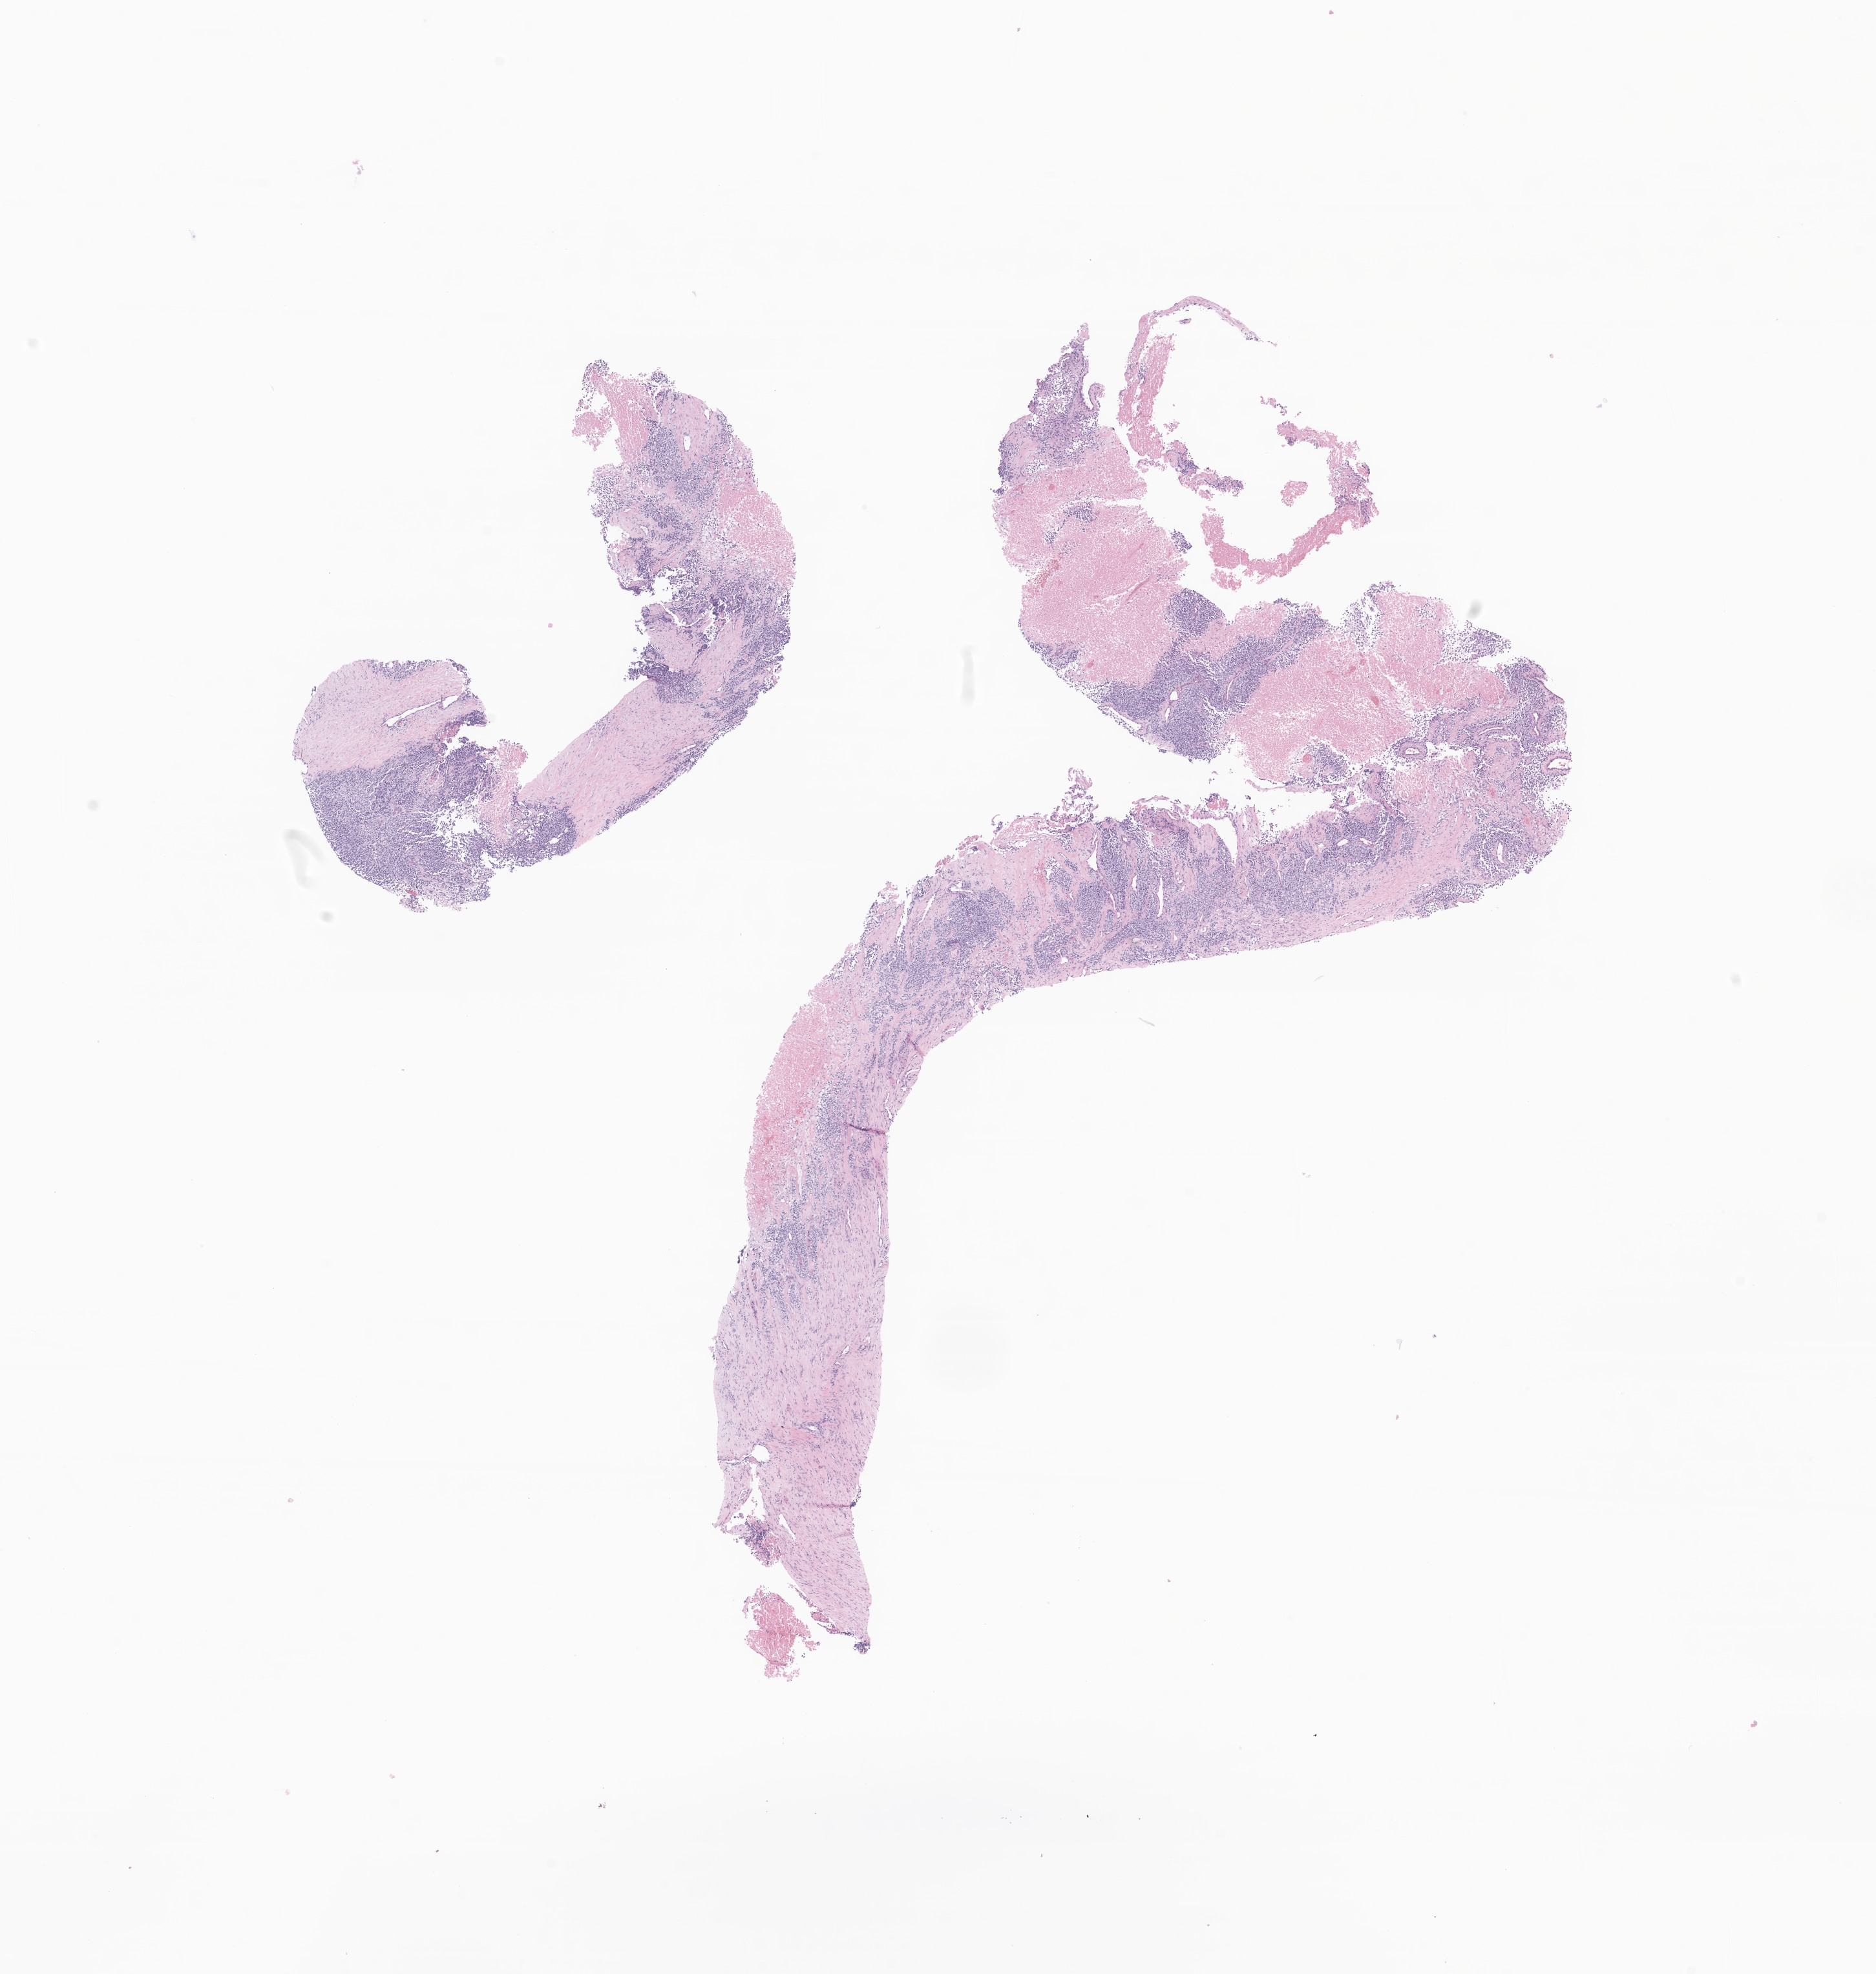
Haematoxylin and eosin whole-slide image of tumor tissue from the soft tissue of upper extremity — whole scanned area (about 12.2 x 12.9 mm) shown as a low-resolution overview. Formalin-fixed paraffin-embedded section. Patient female; age 212 months.
Diagnosis (ICD-O-3 morphology term): Alveolar rhabdomyosarcoma.